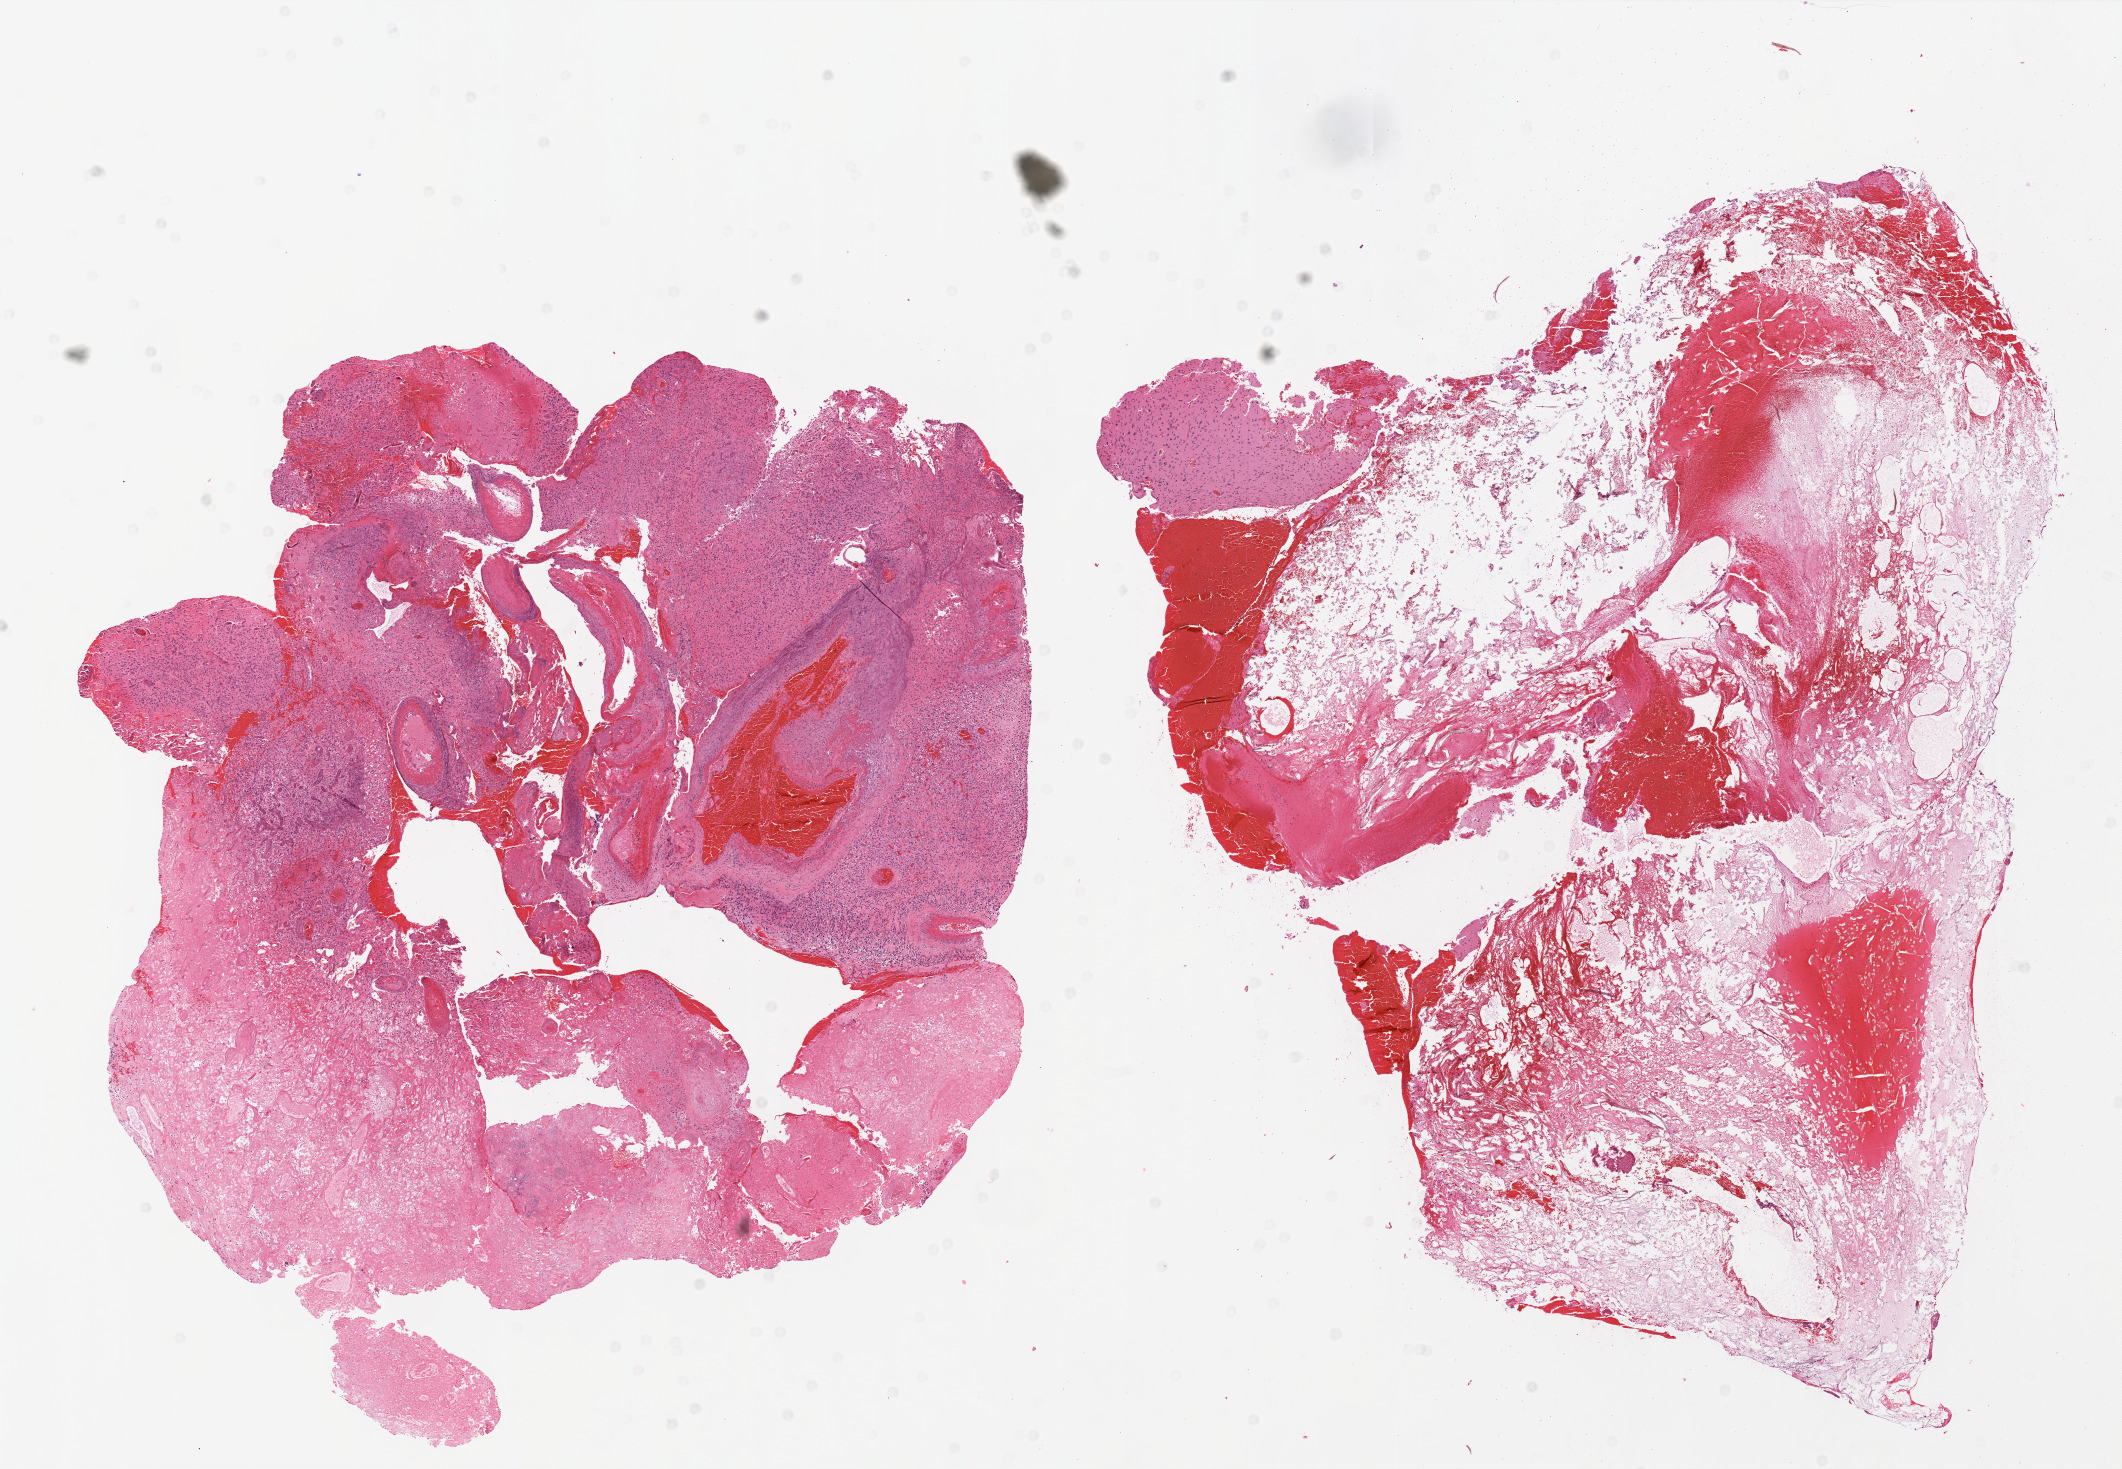
Digitized H&E tissue section (whole slide) — a low-resolution overview of the entire scanned area, about 17.0 x 11.8 mm (from a 20x scan), FFPE section, primary tumour sample from the brain. Male patient; age at initial diagnosis 76 years.
• diagnosis: Glioblastoma